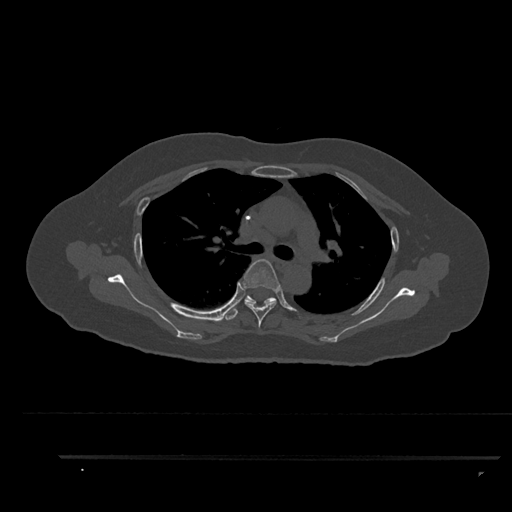
CT including the spine, one axial slice; slice 627 of 797 in the series (ordered by position); reconstruction kernel Br40s/3; bone window (W 1800 / L 400 HU); 0.5 mm slice thickness; 512 × 512 image matrix, field of view 408 × 408 mm. Patient: female, 44 years. From the clinical record (not read from this slice): primary cancer: renal.
Annotated regions visible in this slice (semi-automatically segmented with operator editing):
- T4 vertebra: bounding box (x1, y1, x2, y2) in pixels: (242, 259, 280, 328)
- T5 vertebra: (225, 295, 276, 320)